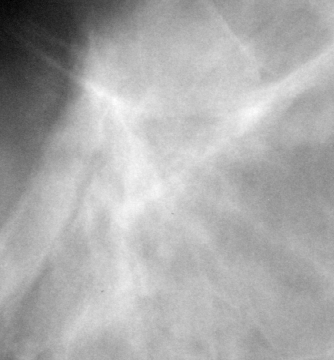
Region of interest cut from a scanned film mammogram (one marked finding); right breast; CC view.
Finding: mass, shape oval, margins spiculated; BI-RADS assessment category 5; pathology result (as recorded, not read from the image): malignant.